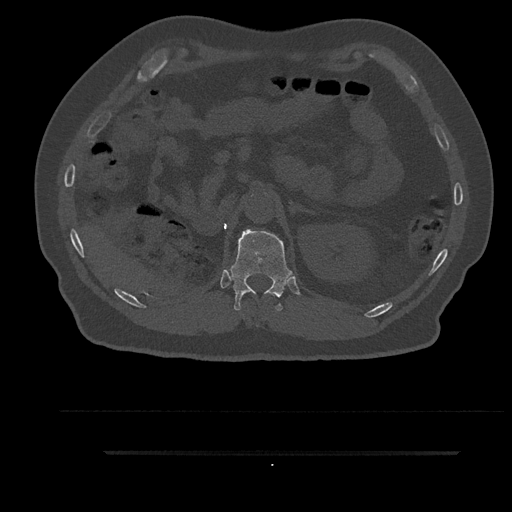
CT including the spine, one axial slice. Slice 251 of 797 in the series (ordered by position). Reconstruction kernel Br40s/3. 120 kVp. Bone window (W 1800 / L 400 HU). 0.5 mm slice thickness. 512 × 512 image matrix. Patient: male, 63 years. Case-level facts recorded for this patient, not image findings: primary cancer: renal; vertebrae with lytic lesions (as recorded): T8.
Annotated regions visible in this slice (semi-automatically segmented with operator editing):
- T12 vertebra: box from (x=227, y=228) to (x=292, y=311) px